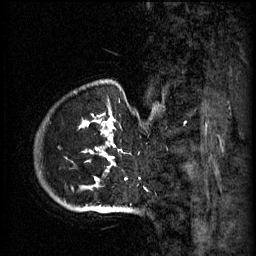
Breast MRI (dynamic contrast-enhanced), one sagittal slice; slice 53 of 60 in the series (ordered by position); 3 images stored at this slice position (order not interpretable as contrast timing); 1.5 T; TE 4.2 ms, TR 11 ms; 256 × 256 image matrix. Patient: female, 51 years.
Structures marked on this image (semi-automatic segmentation, software-assisted and operator-edited):
- analysis volume of interest (the breast-tissue region the enhancement analysis was run in; not a lesion): bounding box <48,82,161,197> (left, top, right, bottom; pixels)
- tumour enhancement mask (voxels above the 70 % enhancement threshold inside the analysis volume of interest): <85,114,127,187>